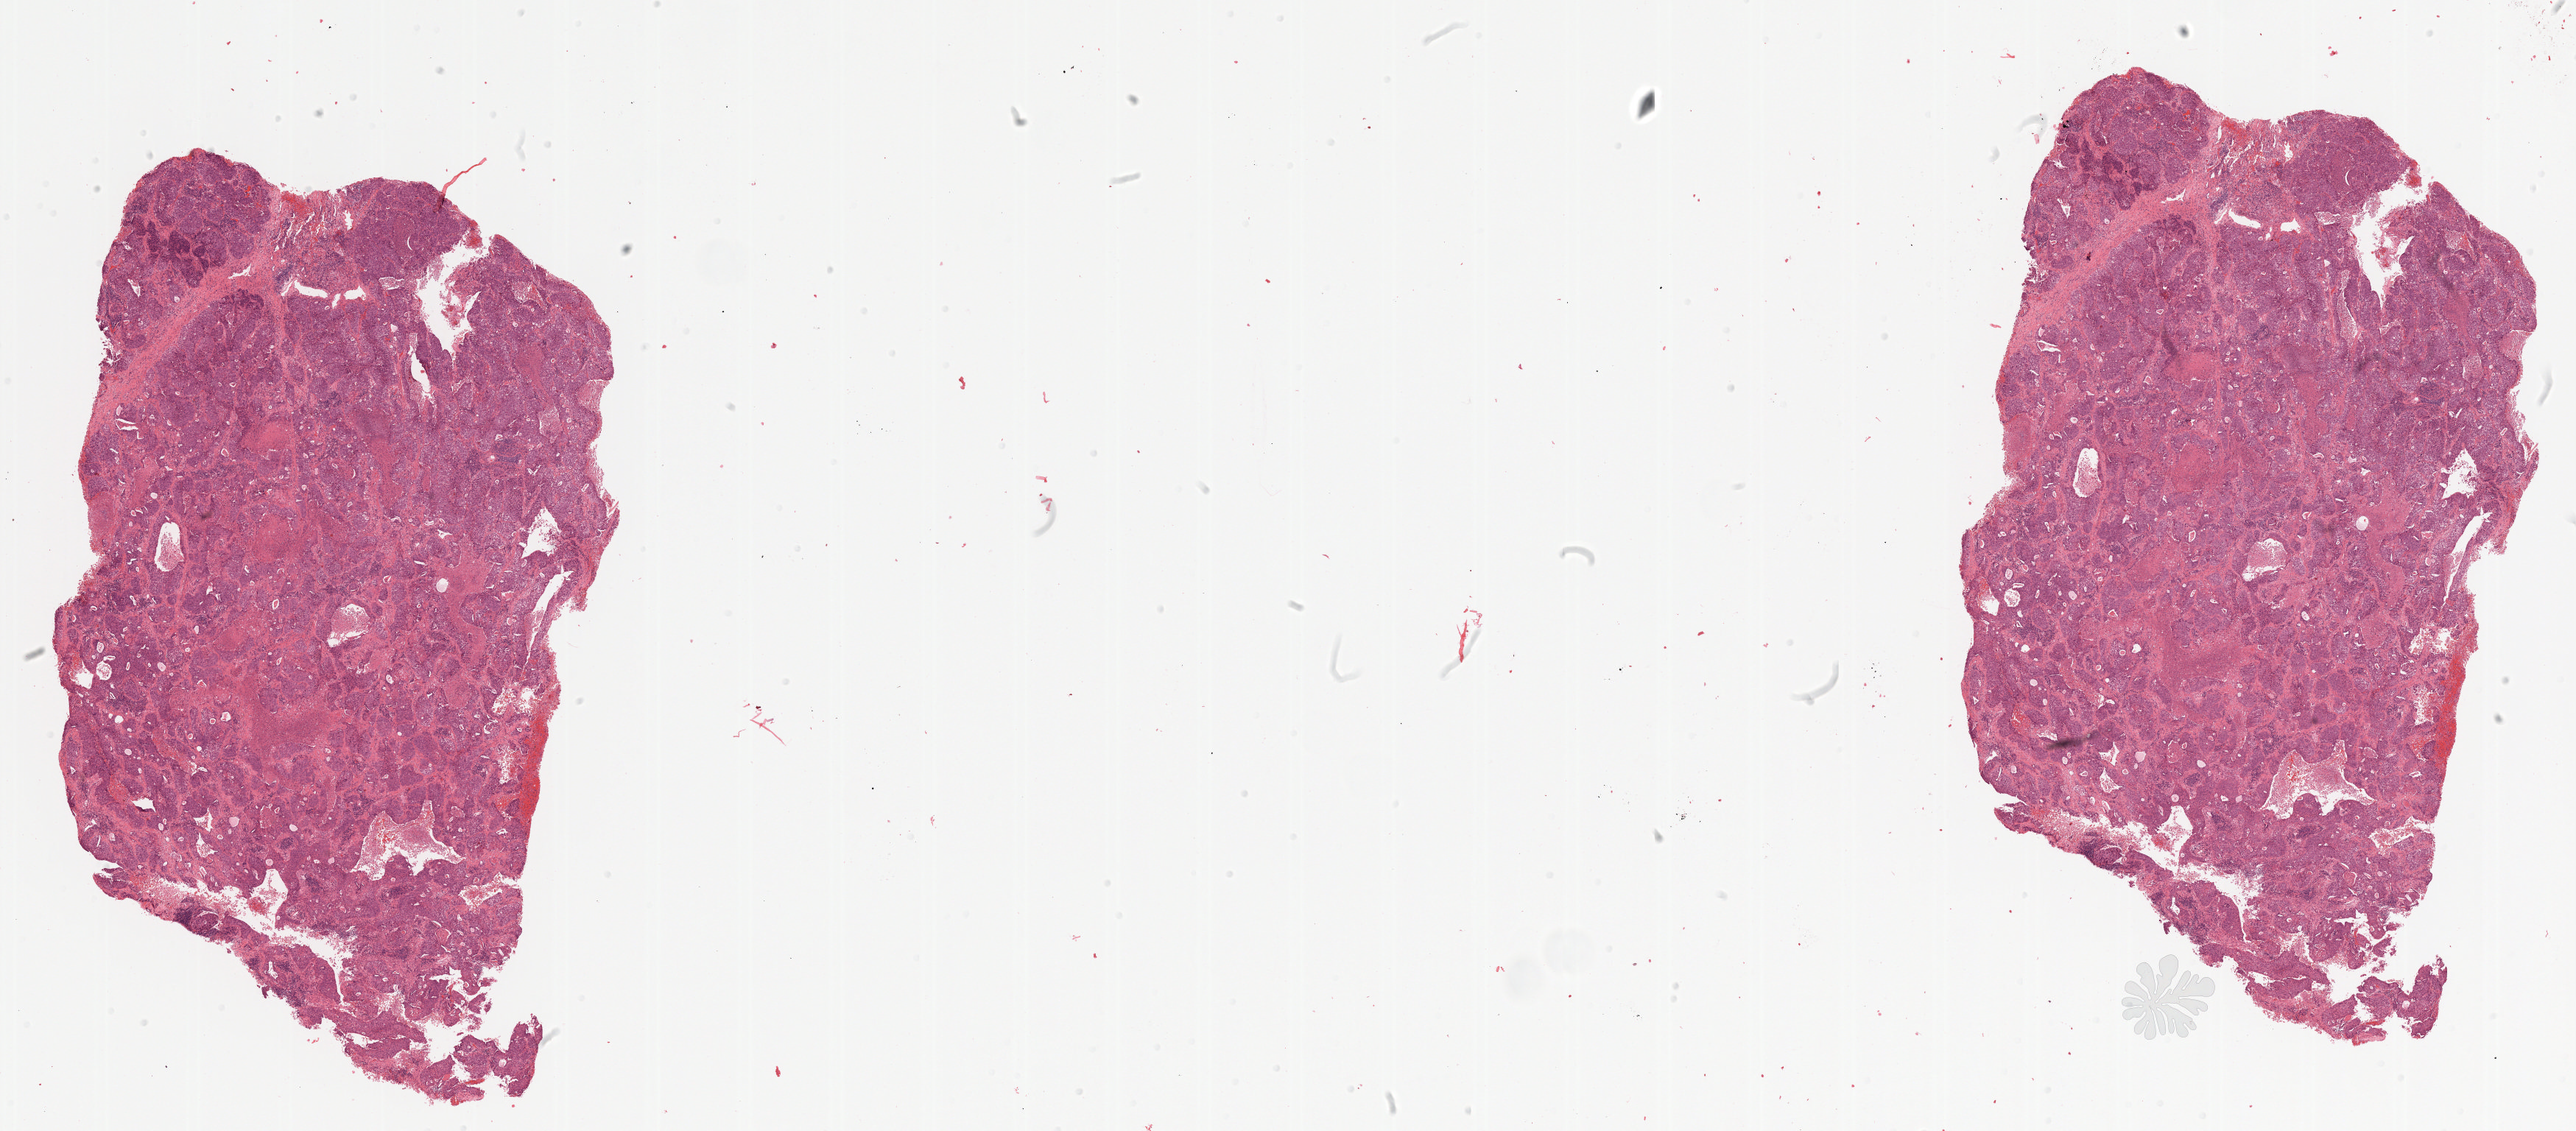
Whole-slide histology image, H&E-stained — a low-resolution overview of the entire scanned area, about 28.0 x 12.3 mm; FFPE section; lung, primary tumour sample. Male, age 65 years at initial diagnosis.
* diagnosis: Squamous cell carcinoma, NOS
* AJCC pathologic stage: IIIA (6th edition)